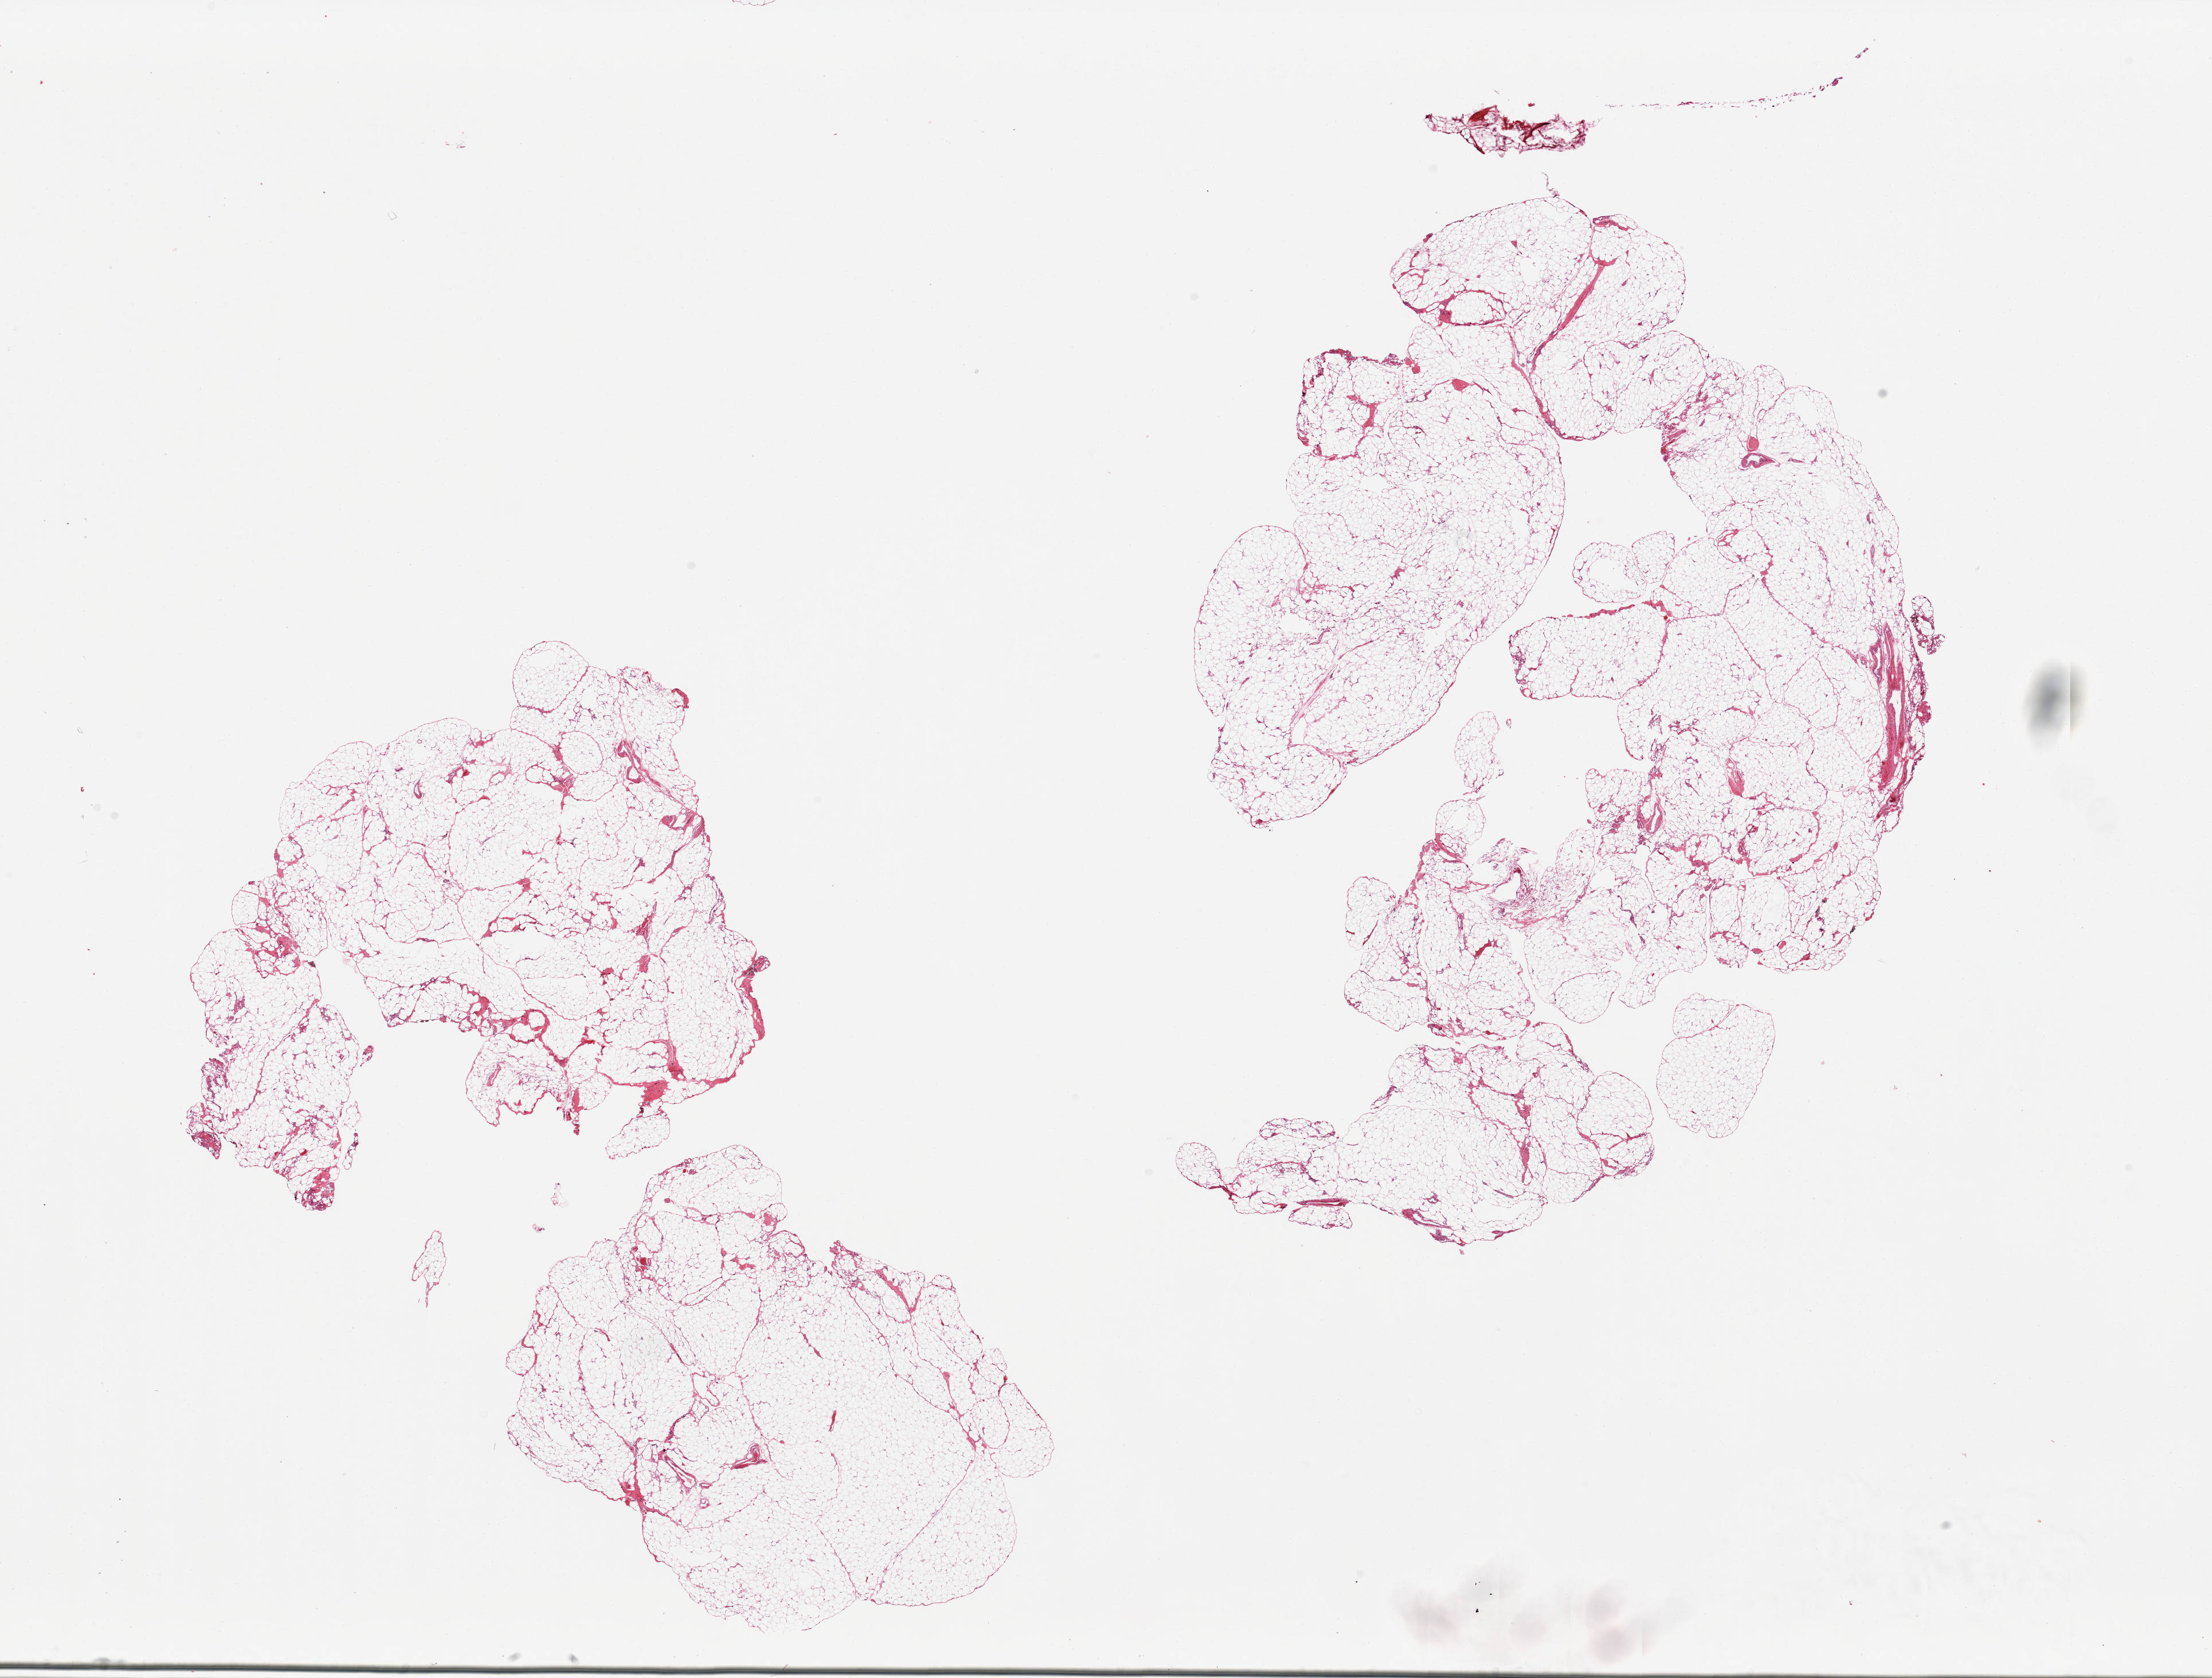
H&E whole-slide image, brightfield, low-resolution overview of the scanned area, about 30.5 x 23.1 mm. PAXgene-fixed, paraffin-embedded tissue. Sampled site (target tissue): omentum. Donor tissue sample. Donor: male.
Pathologist's review note for this sample: 2 pieces, ~5% fibrovascular tissue.